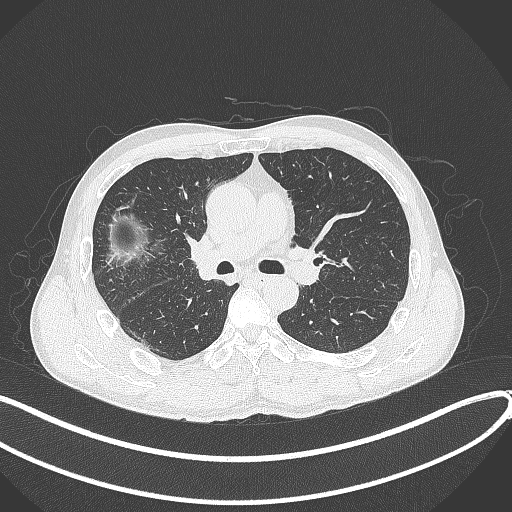
Chest CT, one axial slice. Position 231 of 409 along the scan axis. 120 kVp. Lung window (W 1500 / L -600 HU). 1 mm slice thickness. 512 × 512 image matrix. Male patient, age 53 years. Case-level facts recorded for this patient, not image findings: clinical TNM (as recorded): T1b N0 M0.
Annotated regions visible in this slice (bounding box drawn by a radiologist):
- lung tumour (recorded histology: squamous cell carcinoma): box from (x=182, y=229) to (x=223, y=283) px